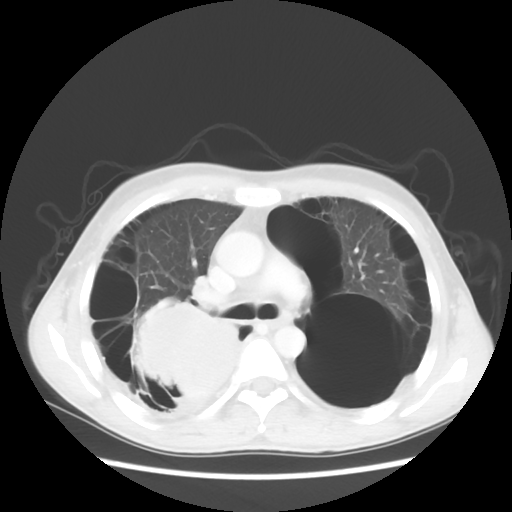
Chest CT, one axial slice. Slice 35 of 56 in the series (ordered by position). Lung window (W 1500 / L -600 HU). 5 mm slice thickness. 512 × 512 image matrix, field of view 351 × 351 mm. Patient: male, 41 years. From the clinical record (not read from this slice): clinical TNM (as recorded): T4 N0 M1a; histopathological grade: G3.
Outlined on this slice (rectangle marked by the reading radiologist):
- lung tumour (recorded histology: large cell carcinoma): bounding box [x1, y1, x2, y2] px = [131, 298, 259, 424]